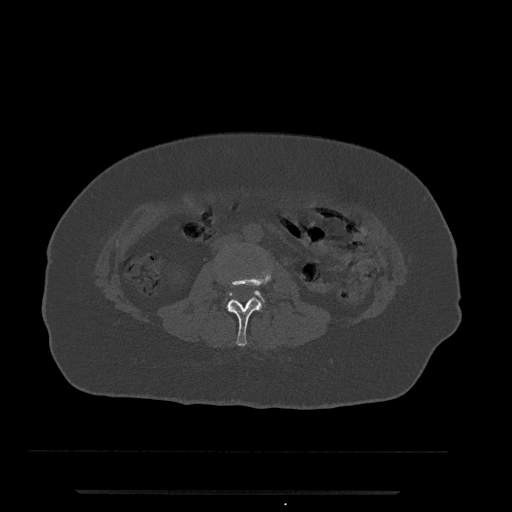
CT including the spine, one axial slice. Slice 11 of 797 in the series (ordered by position). 120 kVp. Bone window (W 1800 / L 400 HU). 512 × 512 image matrix. Patient: female, 51 years. Case-level facts recorded for this patient, not image findings: primary cancer: neuro.
Annotated regions visible in this slice (semi-automatic segmentation, software-assisted and operator-edited):
- L2 vertebra: bounding box [x1, y1, x2, y2] px = [218, 257, 272, 346]